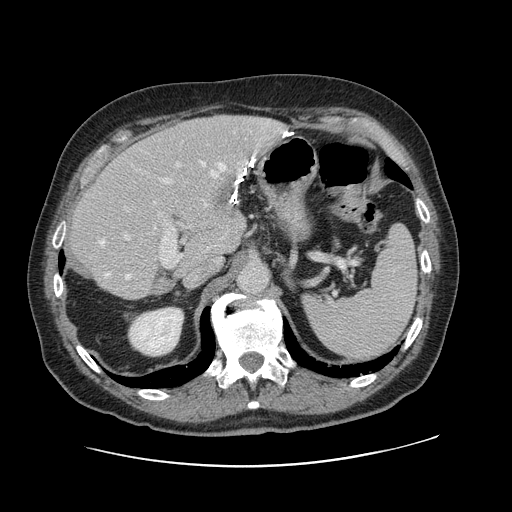
Contrast-enhanced abdominal CT, one axial slice; slice 76 of 138 in the series (ordered by position); intravenous contrast given; soft-tissue window (W 400 / L 40 HU); 512 × 512 image matrix, field of view 402 × 402 mm. Male patient, age 71 years. From the clinical record (not read from this slice): diagnosis: colorectal cancer liver metastases, imaged before liver resection.
Outlined on this slice (expert manual segmentation):
- hepatic veins: bounding box (x1, y1, x2, y2) in pixels: (99, 156, 255, 279)
- liver: (71, 116, 285, 300)
- planned liver remnant (the part of the liver to remain after resection): (71, 149, 233, 300)
- portal vein (with intrahepatic branches): (124, 162, 183, 267)
- liver metastasis: (209, 174, 234, 214)